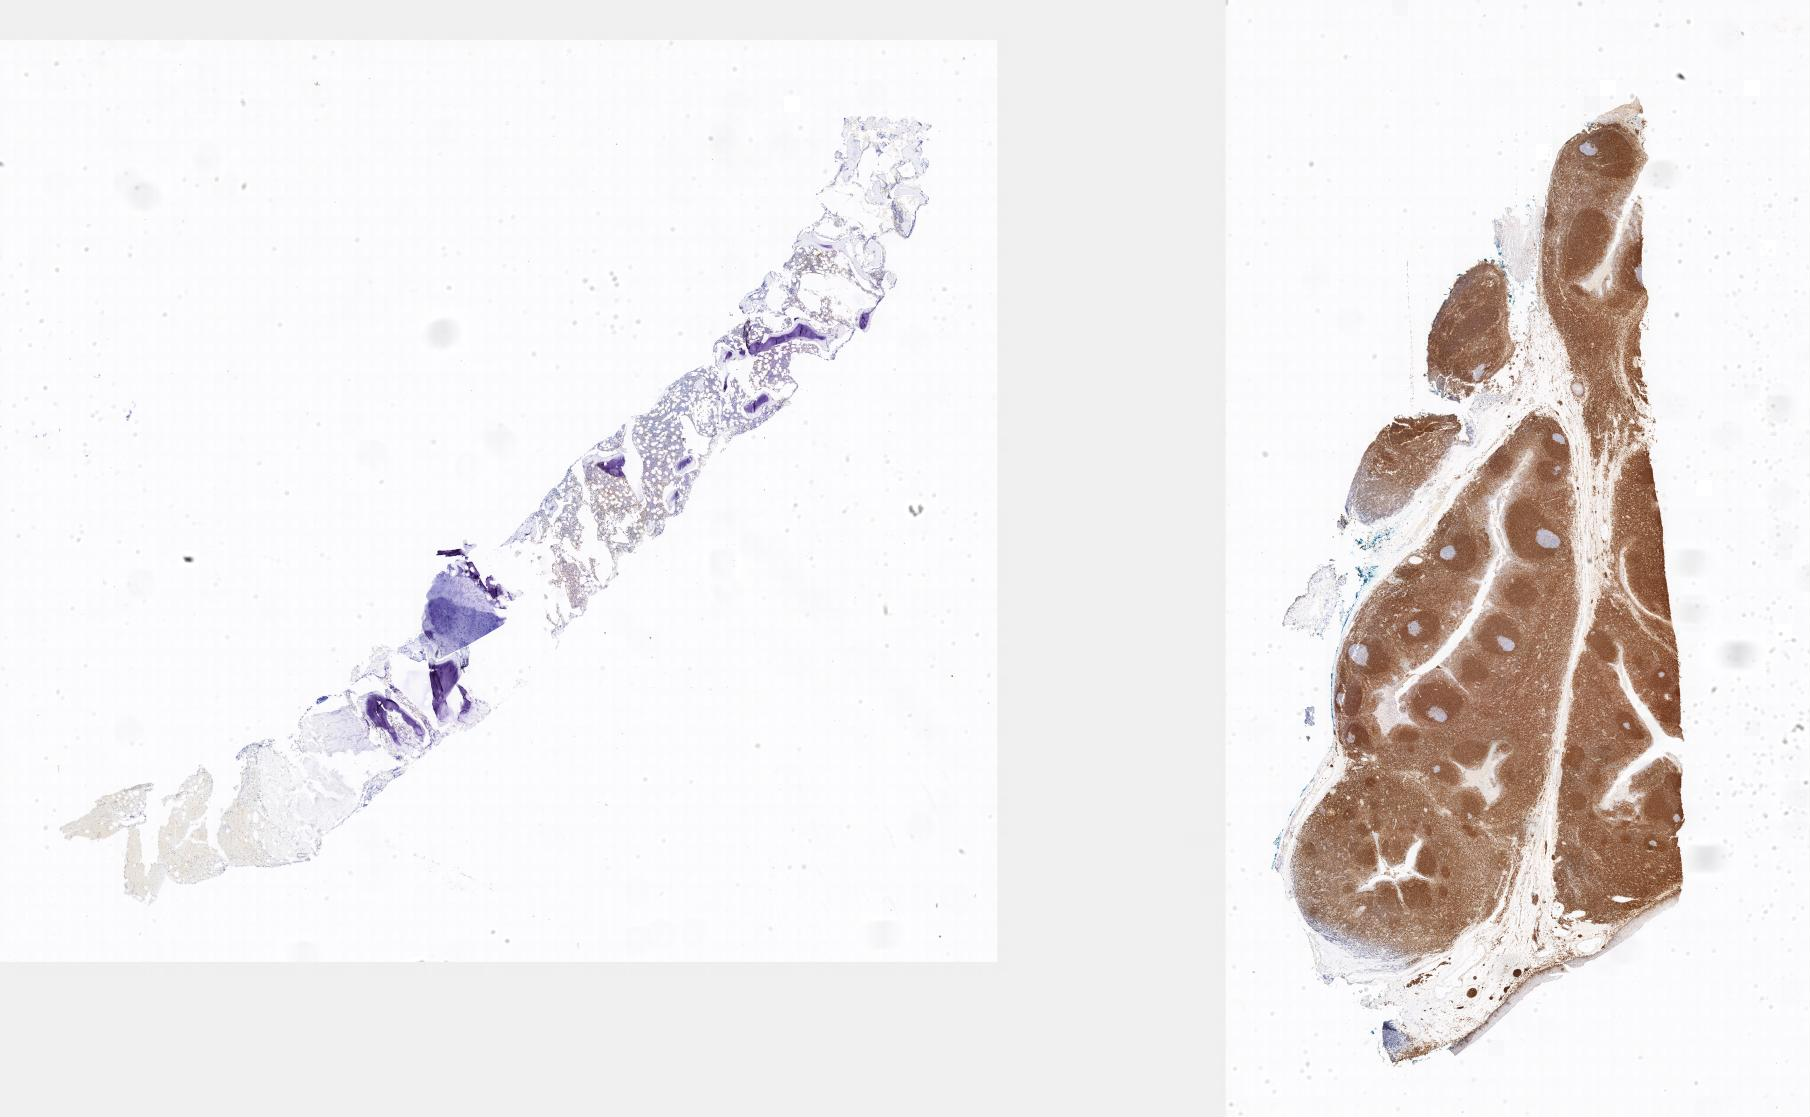
IHC for BCL2, whole-slide image, whole scanned area shown as a low-resolution overview, specimen: tumor tissue, anatomic site: bone marrow. Patient: male, 15 years old.
• diagnosis: Burkitt lymphoma, NOS